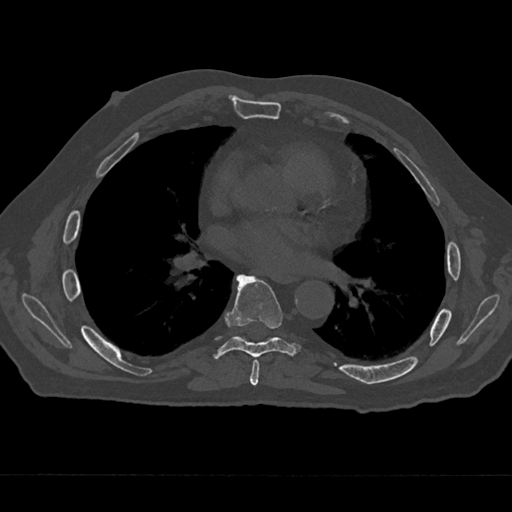
CT including the spine, one axial slice. Slice 371 of 797 in the series (ordered by position). Reconstruction kernel Br40s/3. Bone window (W 1800 / L 400 HU). 0.5 mm slice thickness. 512 × 512 image matrix. Male patient, age 75 years. Case-level facts recorded for this patient, not image findings: primary cancer: renal; vertebrae with lytic lesions (as recorded): T4.
Annotated regions visible in this slice (semi-automatically segmented with operator editing):
- T6 vertebra: bounding box [x1, y1, x2, y2] px = [250, 359, 260, 386]
- T7 vertebra: [213, 274, 302, 360]